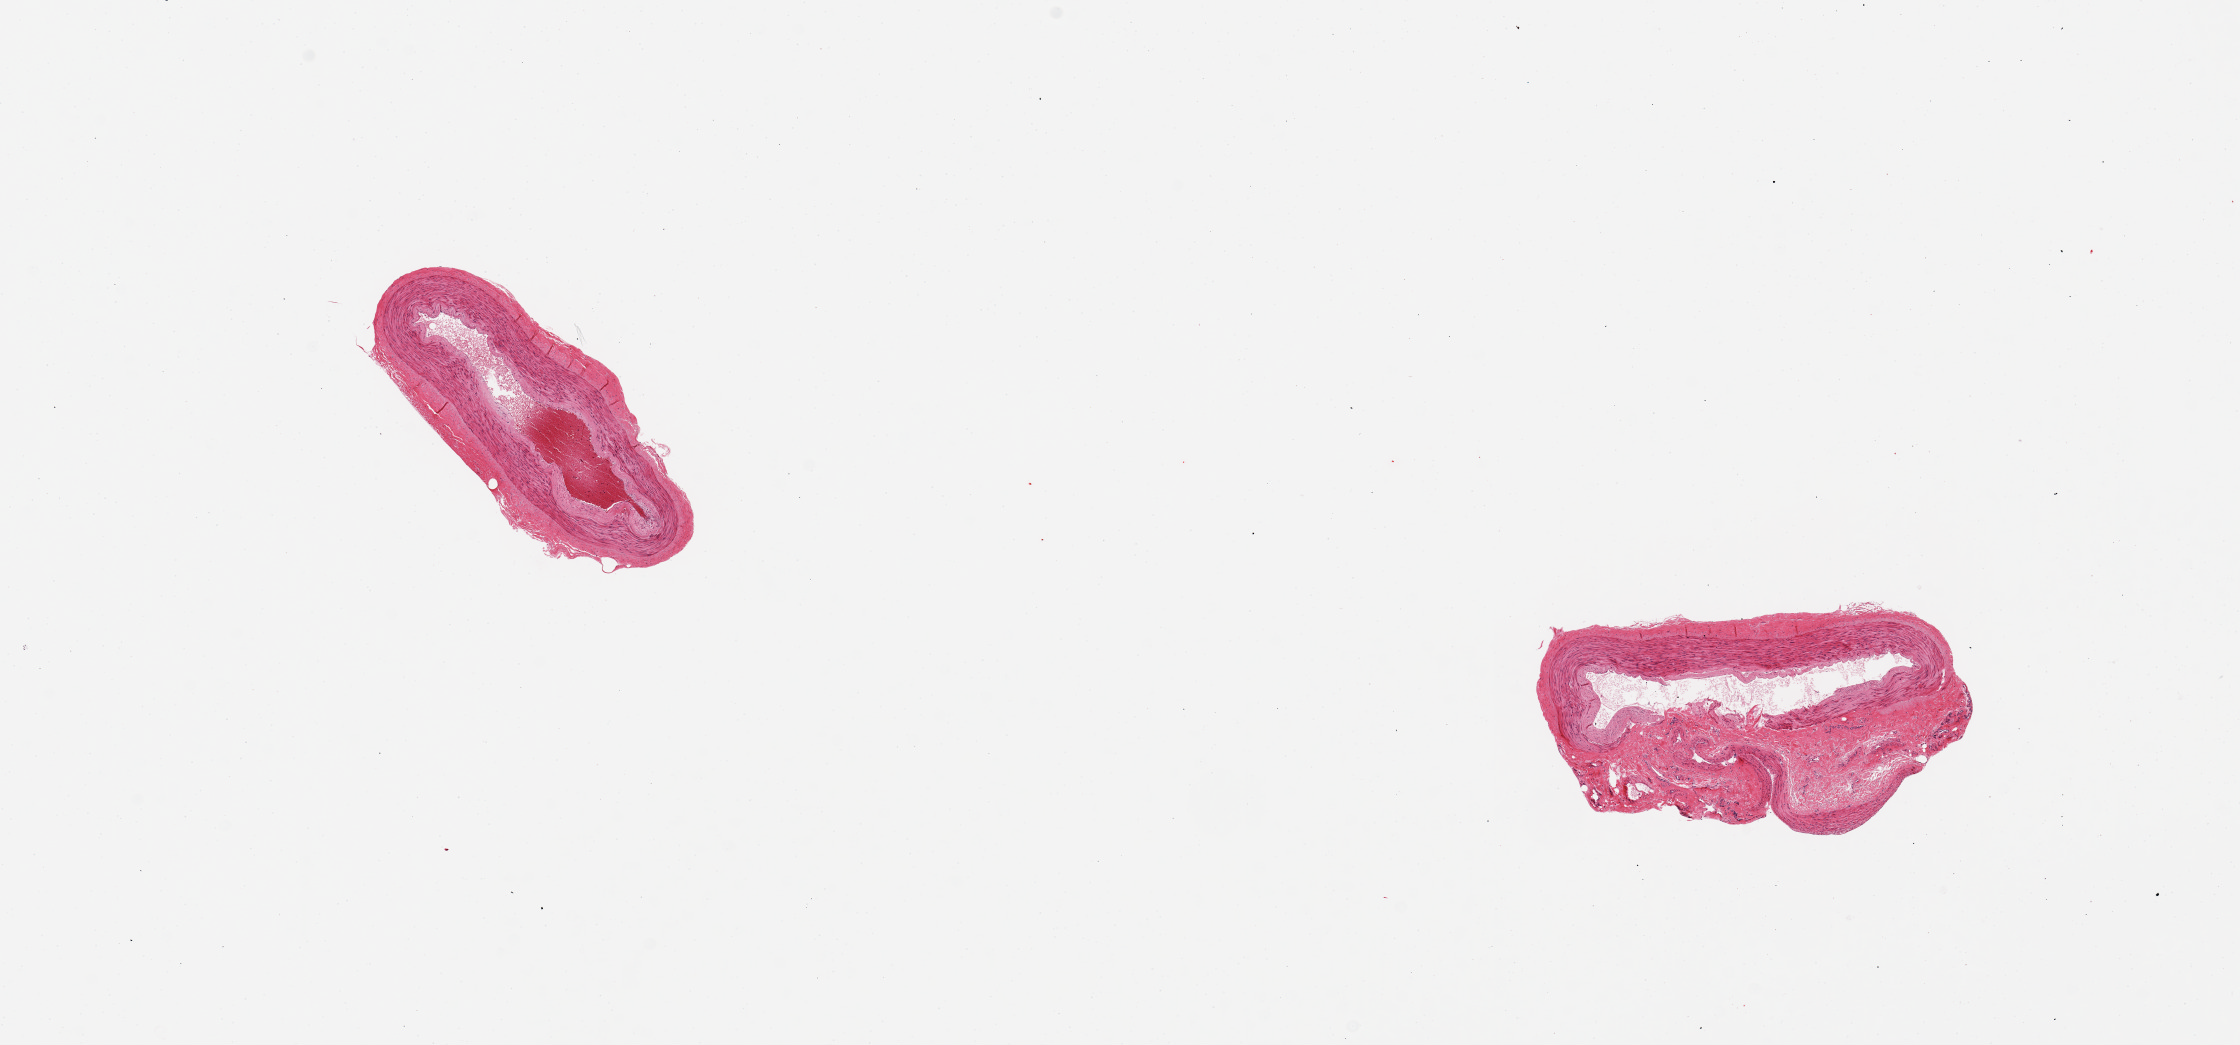
Hematoxylin and eosin (H&E) whole-slide image — low-resolution overview of the scanned area, about 17.7 x 8.3 mm (slide scanned at 20x). PAXgene-fixed, paraffin-embedded tissue. Target tissue: tibial artery. Donor tissue sample. Donor: male.
* reviewer comment on this tissue sample: 2 pieces